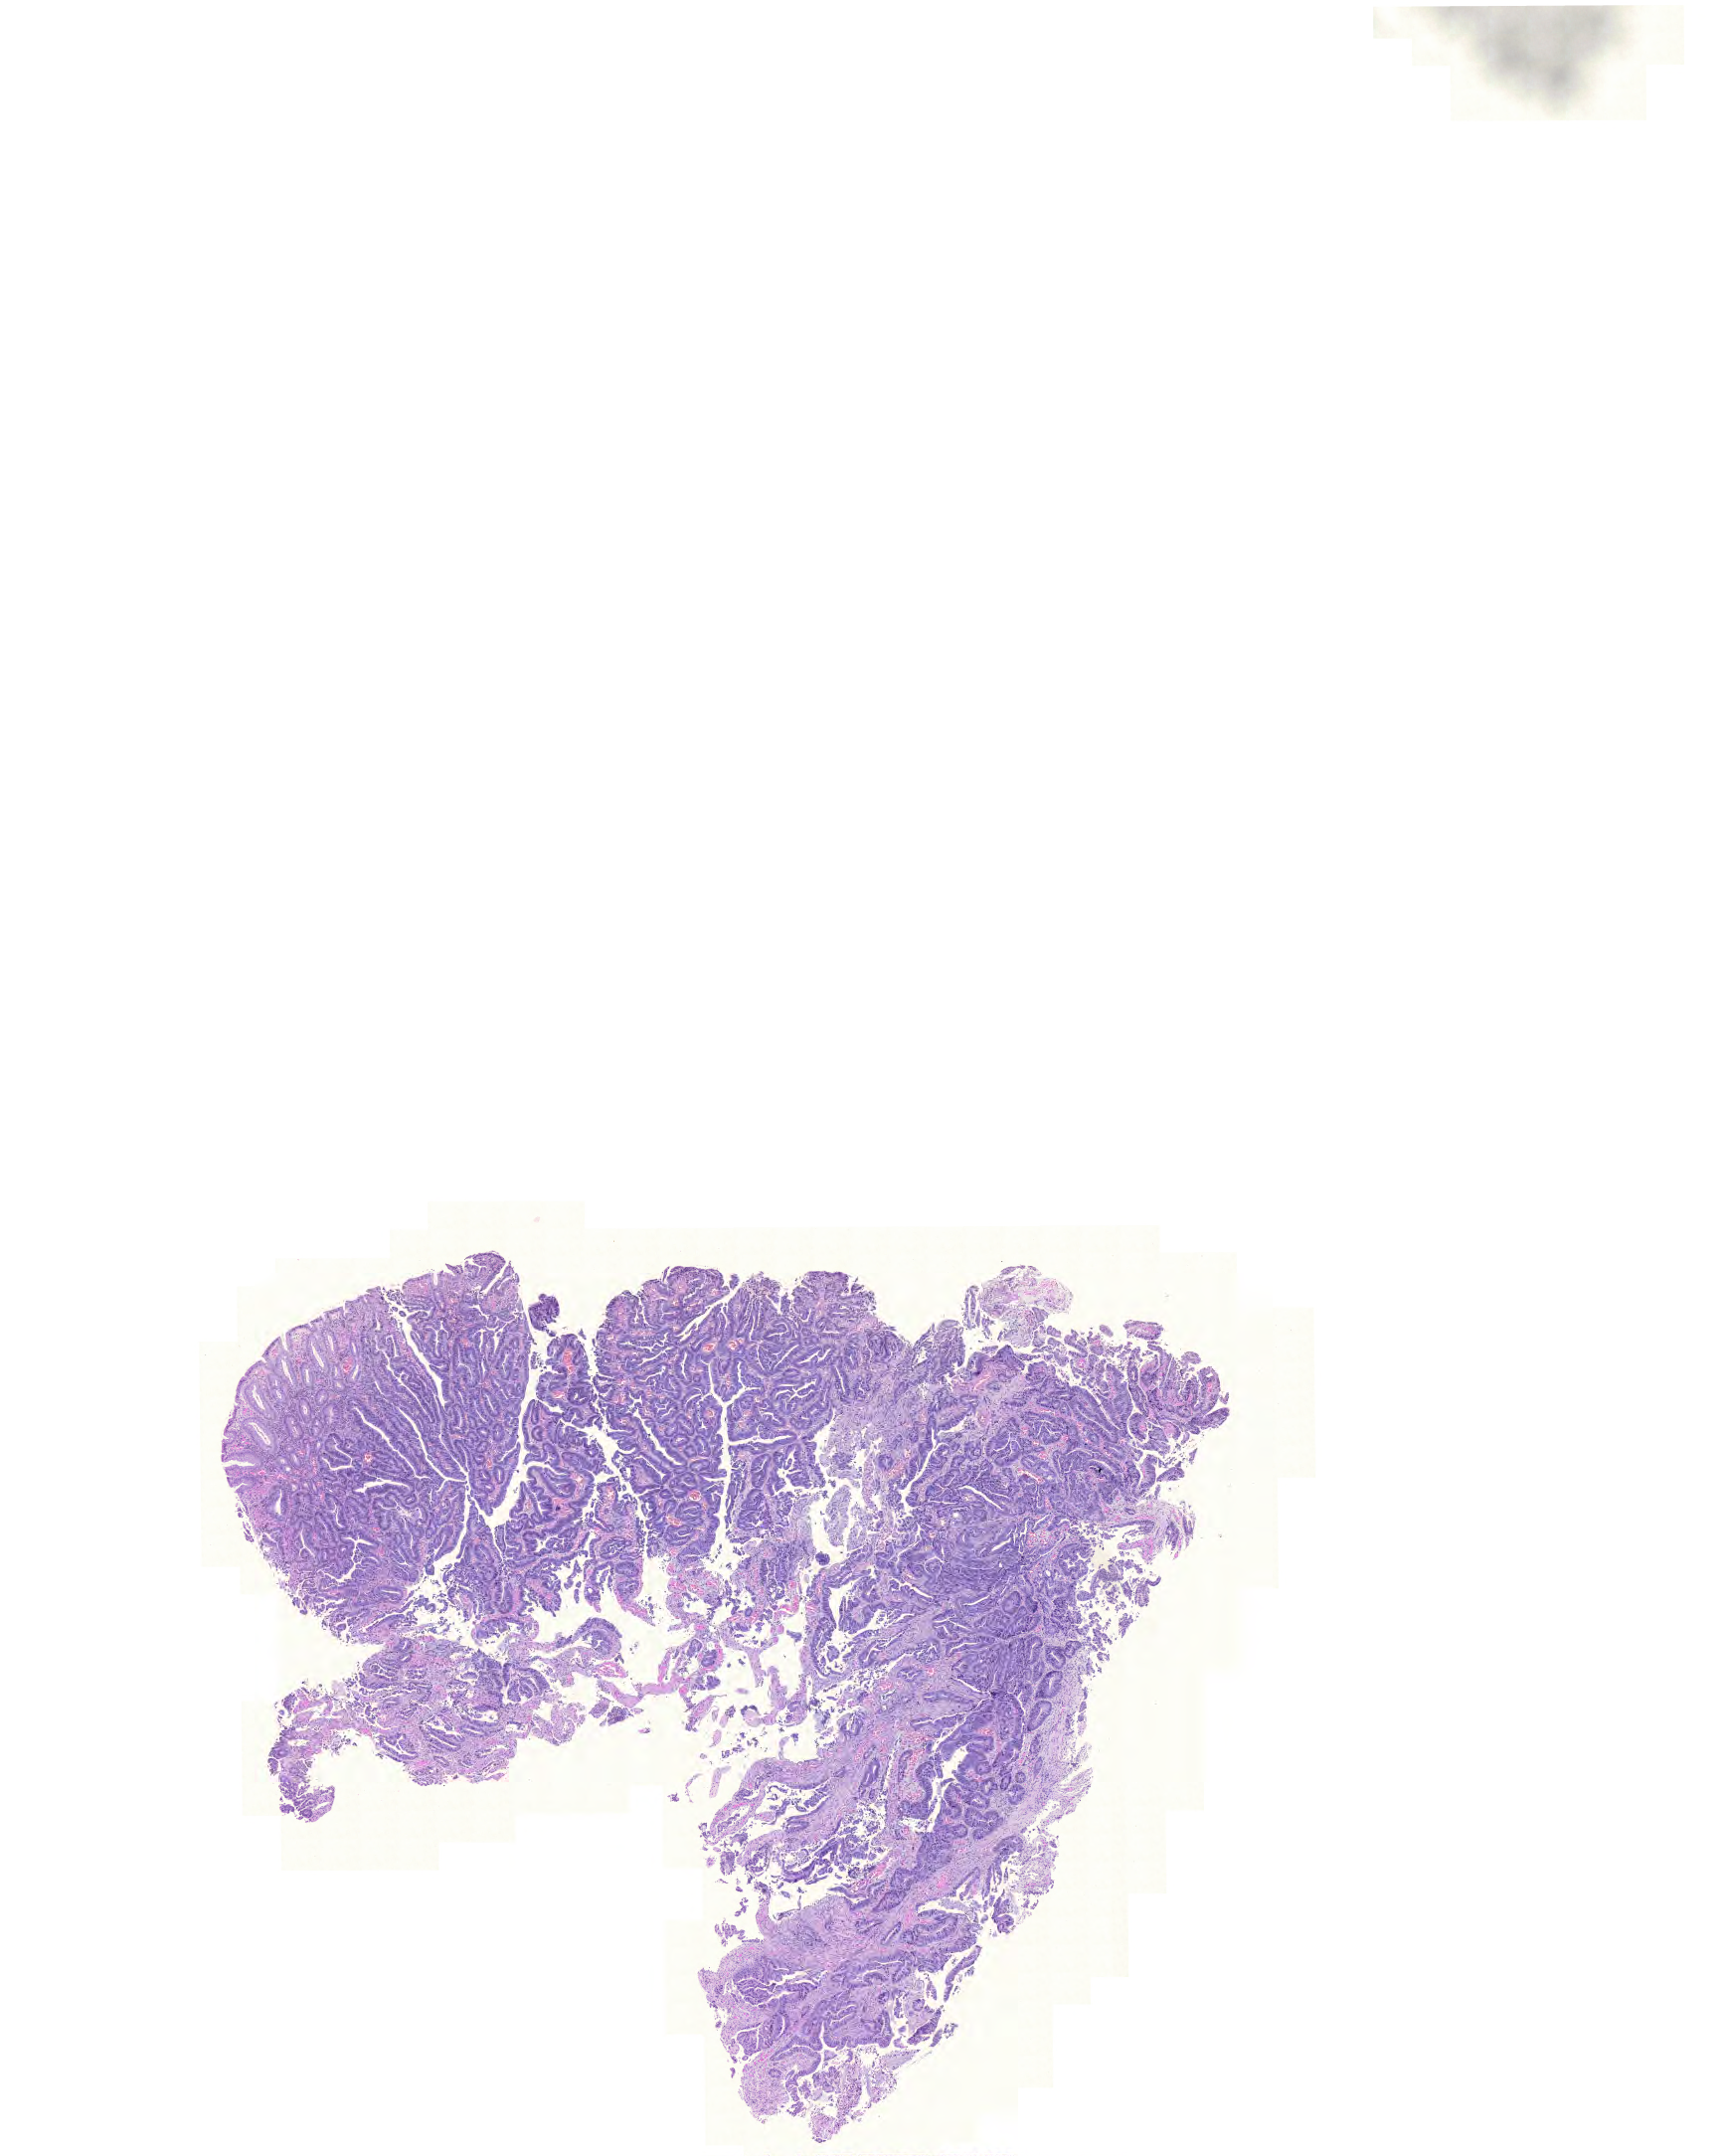
Whole-slide histology image, H&E, a low-resolution overview of the entire scanned area, about 12.9 x 16.1 mm (slide scanned at 20x). Formalin-fixed paraffin-embedded (FFPE) diagnostic section. Colon, primary tumour sample. Patient: male, age at initial diagnosis 51 years.
Histologic diagnosis: Adenocarcinoma, NOS. AJCC pathologic stage: IIIA (6th edition). Lymph nodes positive (case pathology): 2 of 12 examined.